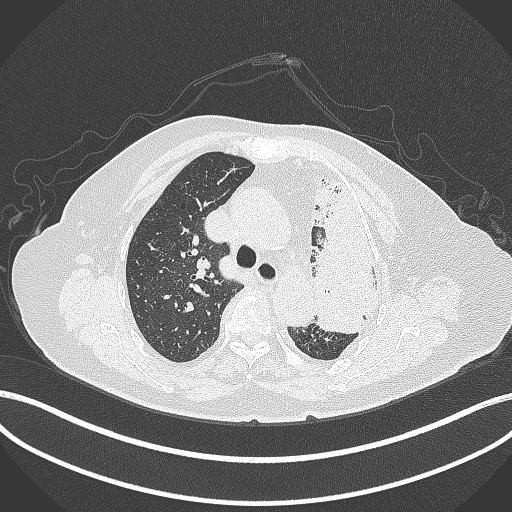
Chest CT, one axial slice; slice 282 of 399 in the series (ordered by position); reconstruction kernel B70f; lung window (W 1500 / L -600 HU); 1 mm slice thickness; 512 × 512 image matrix. Patient: female, 75 years. Case-level facts recorded for this patient, not image findings: clinical TNM (as recorded): T3 N3 M1.
Structures marked on this image (bounding box drawn by a radiologist):
- lung tumour (recorded histology: adenocarcinoma): bounding box (x1, y1, x2, y2) in pixels: (312, 160, 384, 335)